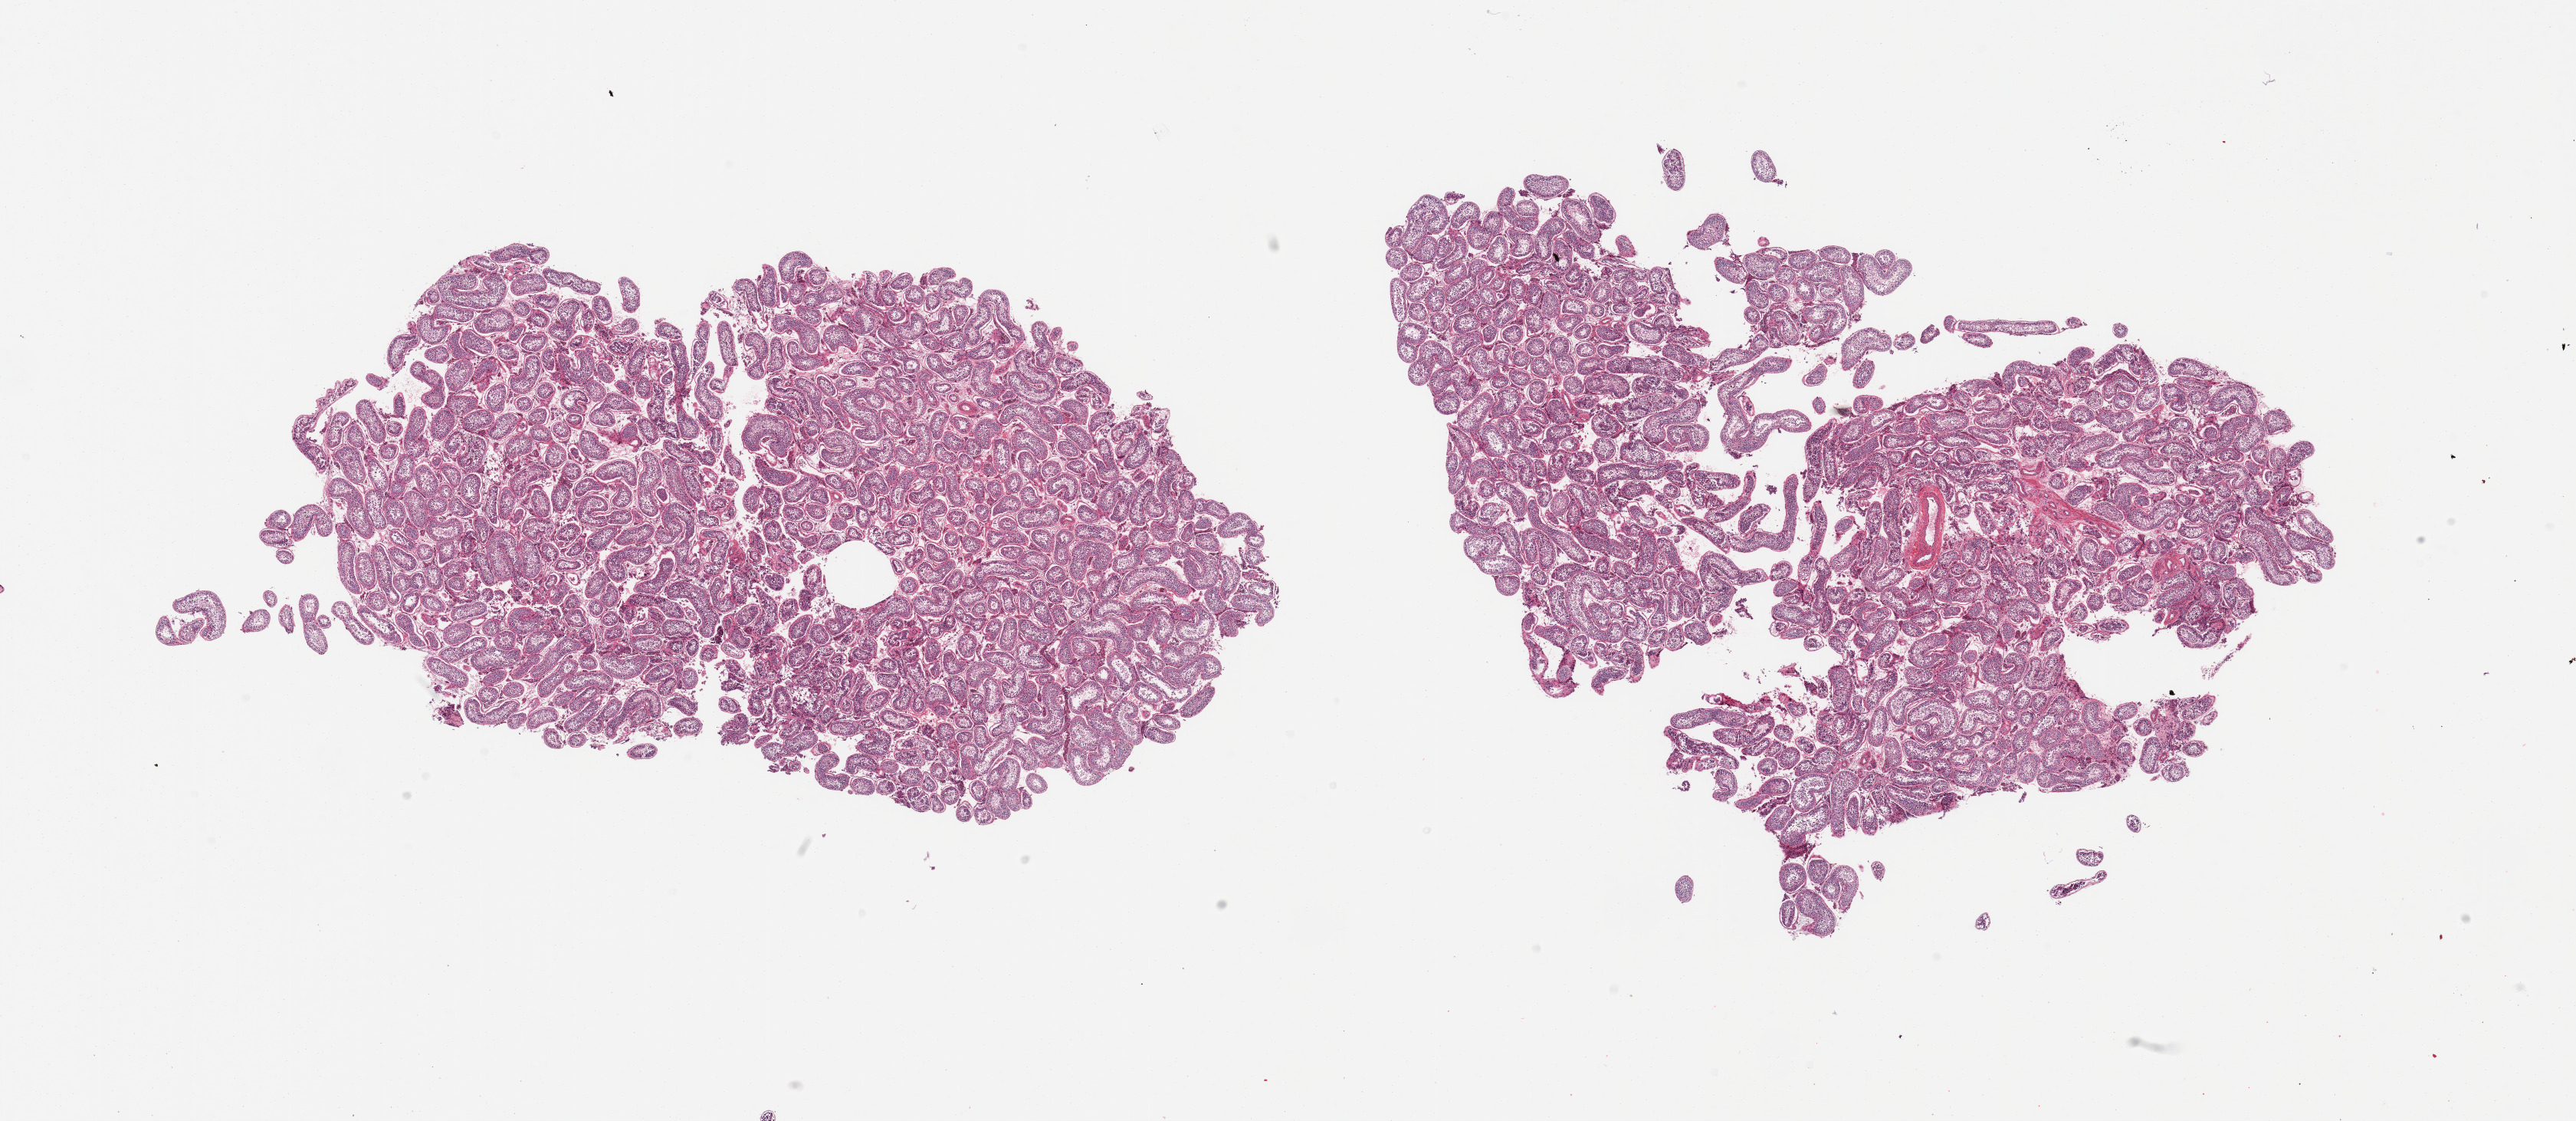
Digitized haematoxylin and eosin-stained section, brightfield, whole scanned area (about 26.6 x 11.6 mm) shown as a low-resolution overview. PAXgene-fixed, paraffin-embedded tissue. Sampled site (target tissue): testis. Donor tissue sample. Male donor.
Reviewer comment on this tissue sample: 2 pieces; spermatogenesis is present.